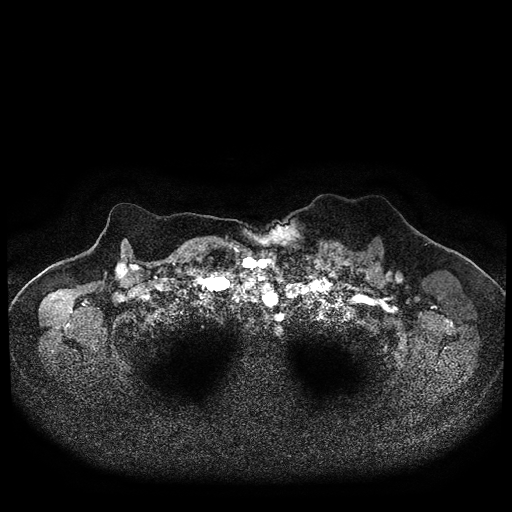
Breast MRI (dynamic contrast-enhanced, multi-phase), one axial slice. Dynamic contrast-enhanced series, time point 2 of 5 at this slice position (early post-contrast). 1.5 T. TE 2.7 ms, TR 5.4 ms. 2 mm slice thickness. 512 × 512 image matrix, field of view 340 × 340 mm. Patient: female, 72 years.
Annotated regions visible in this slice (semi-automatically segmented with operator editing):
- breast lesion (labelled 'tumour' in the annotation; benign lesions carry a separate 'benign' label): bounding box <114,258,129,282> (left, top, right, bottom; pixels)